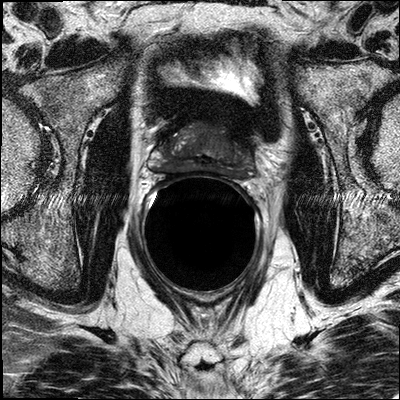
MRI of the prostate; 3 images, each a single mid-volume slice chosen by position (not for content). Treatment context recorded for this patient: No surgery.
Image 1: axial T2-weighted image, series "T2W_TSE_AX", slice 17 of 32, 3 mm slice thickness.
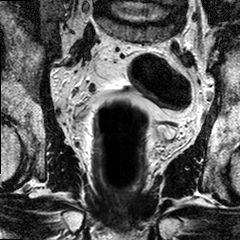
Image 2: coronal T2-weighted image, slice 13 of 24.
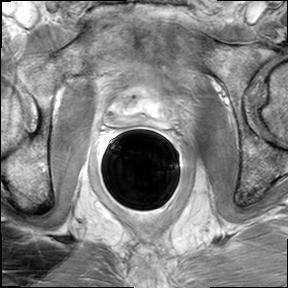
Image 3: DCE (dynamic gadolinium-enhanced) axial slice, slice 17 of 32, dynamic phase 5 of 8.
MRI report (verbatim):
The zonal anatomy is preserved. Maximal craniocaudal diameter is 3.8 cm. Maximal AP diameter 2.4 cm and maximal transverse diameter 4.2 cm. Estimated total gland volume approximately 25 cc, including a prominent middle lobe protruding into the bladder neck. The posterior-lateral peripheral zone and adjacent central gland of the mid 3rd base and apex between 6 and 8 o'clock shows suspicious T2 hypointense signal and rapid wash in and wash out on the dynamic contrast enhanced series. The dominant nodule within the mid 3rd at the junction to the apical 3rd of the prostate at 7 o'clock measures 18 x 12 mm the adjacent capsule is regular, without suspicious signal or enhancement beyond the capsule . Smaller areas with suspicious T2 hyperintense signal and suspicious contrast enhancement are seen in the left peripheral zone, mid-third and base as well as left apex. No evidence of extracapsular extension. No evidence of involvement of the neurovascular bundles on either side. No seminal vesicle infiltration. No suspicious the enlarged obturator or iliac lymph nodes. IMPRESSION: Bilateral prostate cancer, involving base mid 3rd and apical third of the prostate, with dominant nodule in the right posterior lateral peripheral zone and adjacent central gland (7-8 o'clock) as described above. Smaller foci also seen on the left side. No evidence of fracture or prosthetic extension no evidence of involvement of the neural vascular bundles on either side or seminal vesicles. No pelvic lymphadenopathy.

Biopsy pathology report for this patient (as recorded):
PROSTATIC CORE NEEDLE BIOPSIES: 1. RIGHT PZ PROSTATIC ADENOCARCINOMA, 4+3=7/10, INVOLVING APPROXIMATELY 60% OF THE TISSUE SUBMITTED. 2. RIGHT PZ/TZ: PROSTATIC ADENOCARCINOMA, 4+3=7/10, INVOLVING APPROXIMATELY 80% OF THE TISSUE SUBMITTED. 3. RIGHT APEX: PROSTATIC ADENOCARCINOMA, 4+3=7/10, INVOLVING APPROXIMATELY 80% OF THE TISSUE SUBMITTED. 4. LEFT PZ: PROSTATIC ADENOCARCINOMA, 3+4=7/10, INVOLVING APPROXIMATELY 20% OF THE TISSUE SUBMITTED. 5. LEFT PZ/TZ: PROSTATIC TISSUE. NO TUMOR IDENTIFIED. 6. LEFT APEX: PROSTATIC TISSUE. NO TUMOR IDENTIFIED.